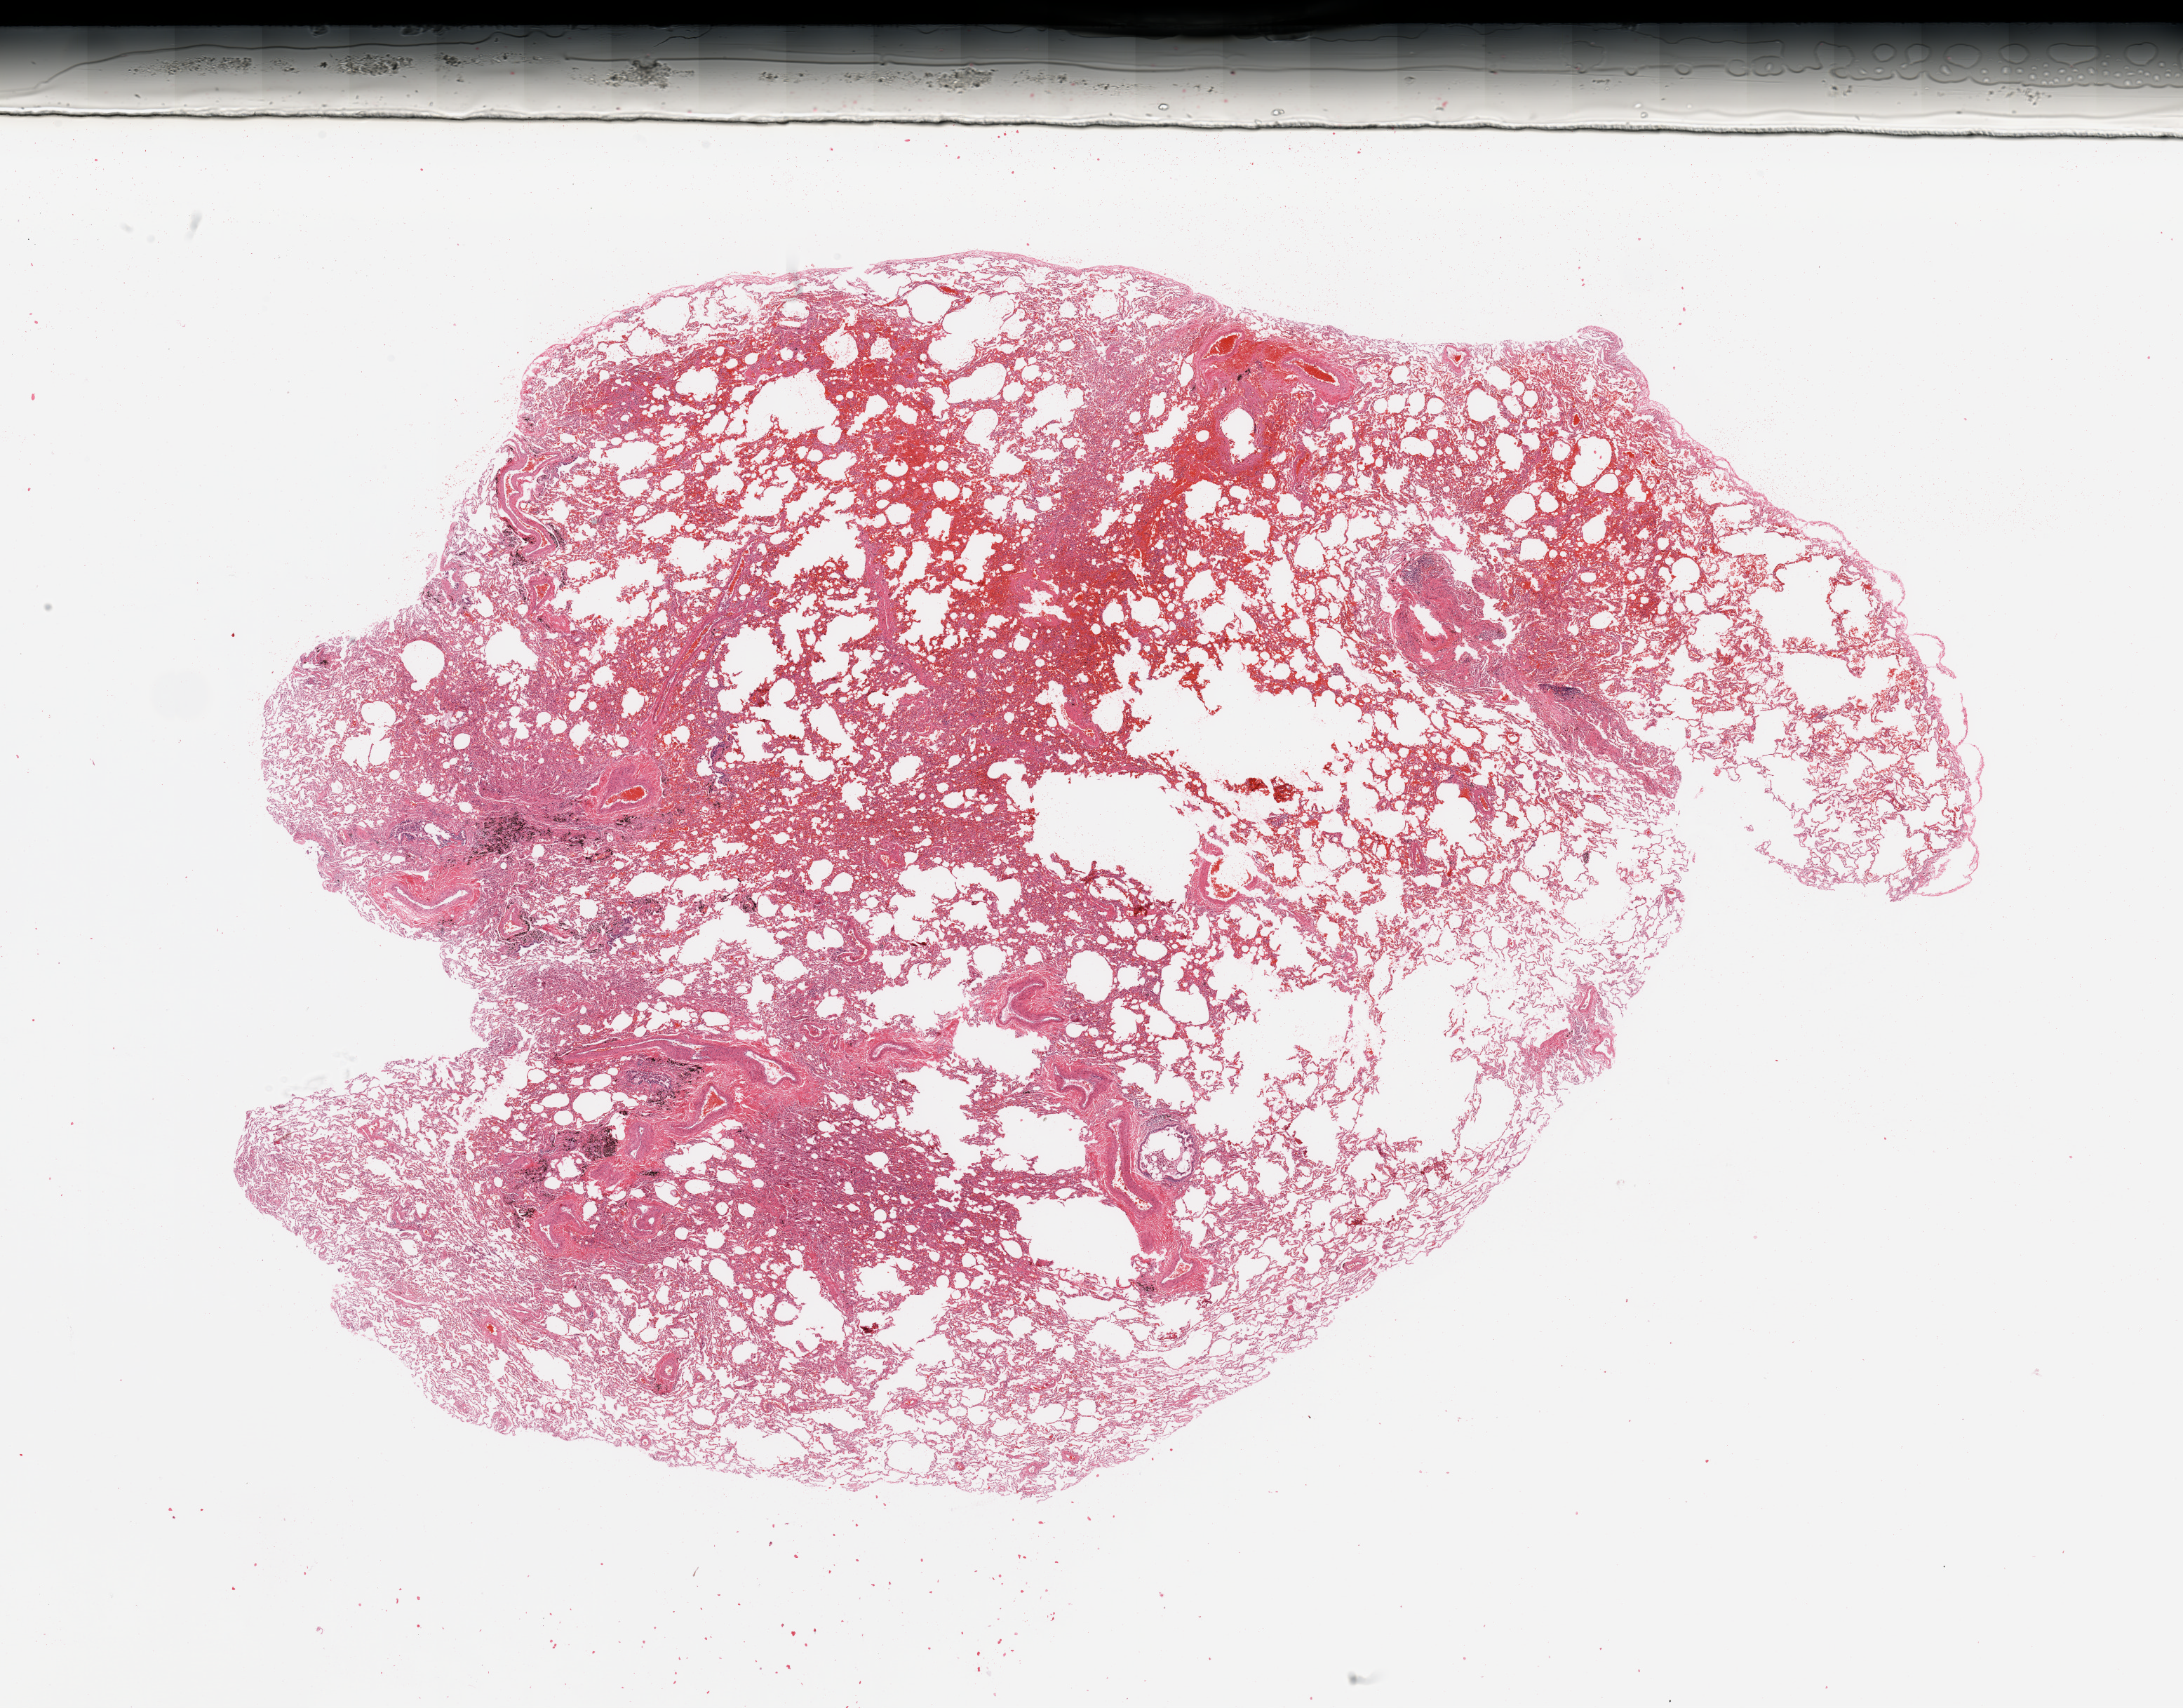
H&E-stained whole-slide image, shown as a low-resolution overview of the whole scanned area (about 24.6 x 19.3 mm, from a 20x scan), normal (non-tumour) tissue sample, sampled site: lung. Patient: male, age 48 years.
This section: normal (non-tumour) tissue from the same patient. Patient diagnosis: Adenocarcinoma, NOS.